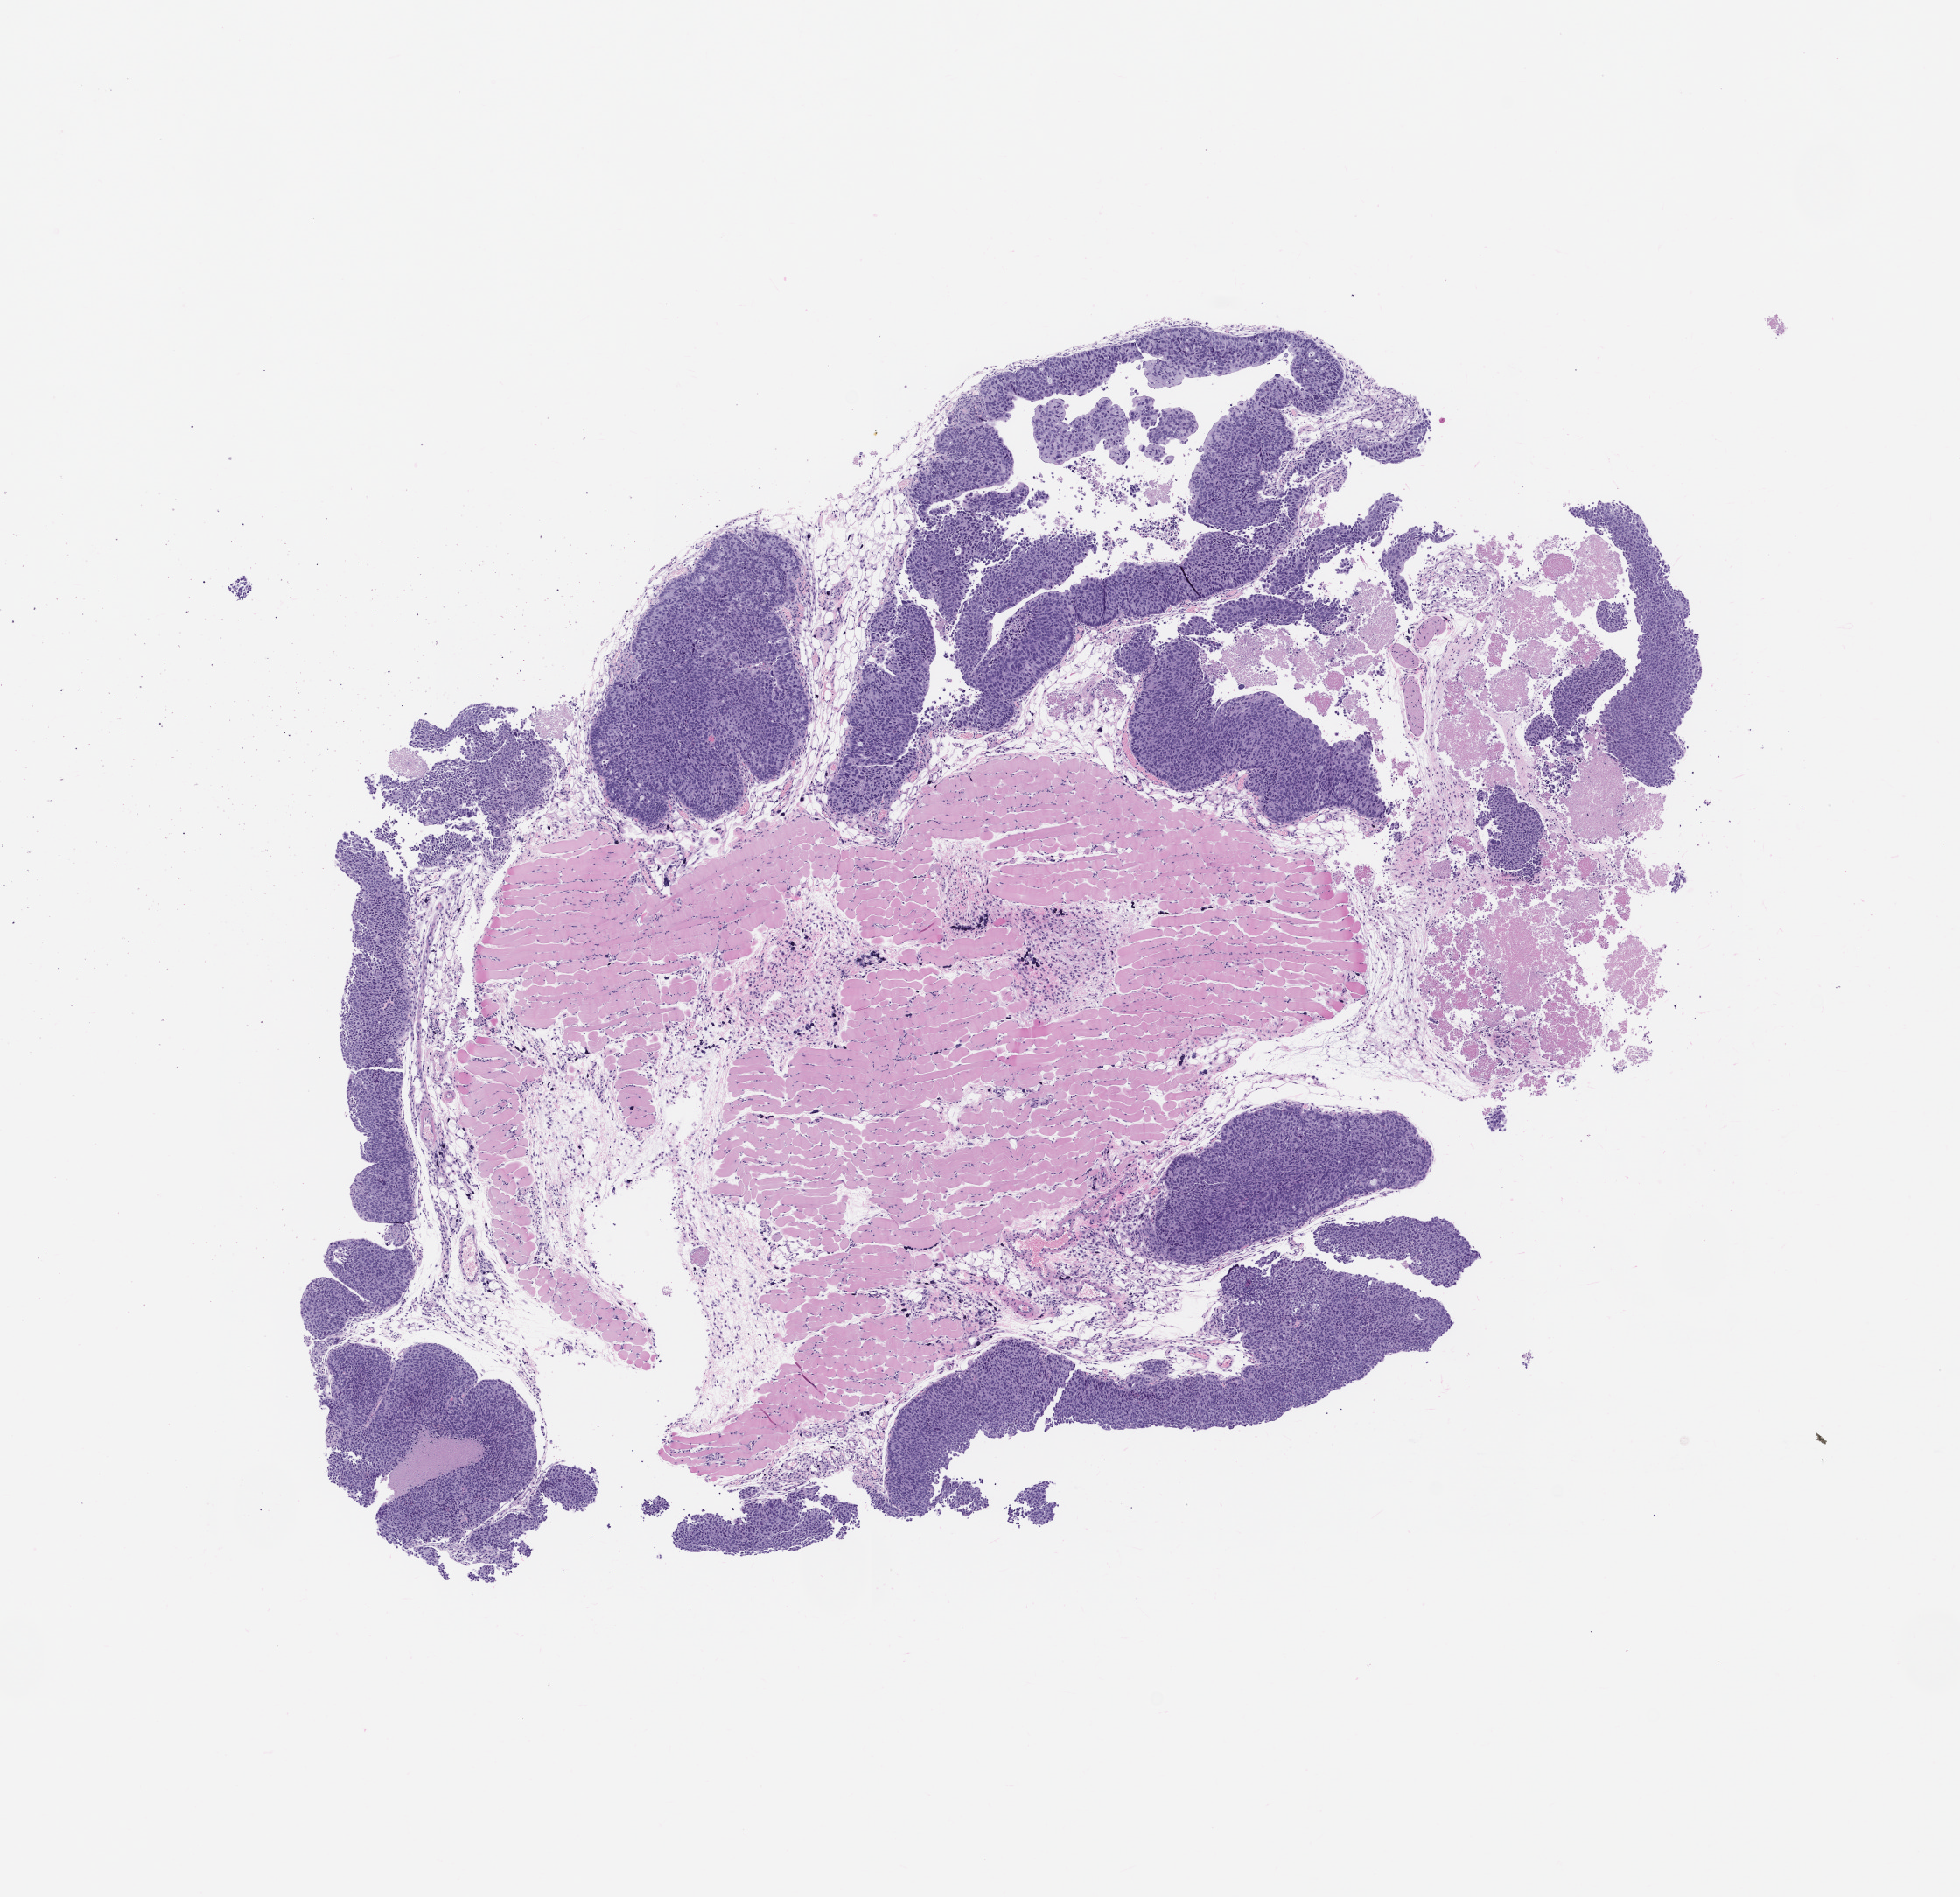
Haematoxylin and eosin whole-slide image of a patient-derived xenograft (PDX) tumor grown in a mouse, passage 2 — a low-resolution overview of the entire scanned area, about 9.0 x 8.7 mm. Formalin-fixed, paraffin-embedded (FFPE) tissue. Tumor site category: gastrointestinal tract.
Originating patient diagnosis: Gastric Adenocarcinoma.